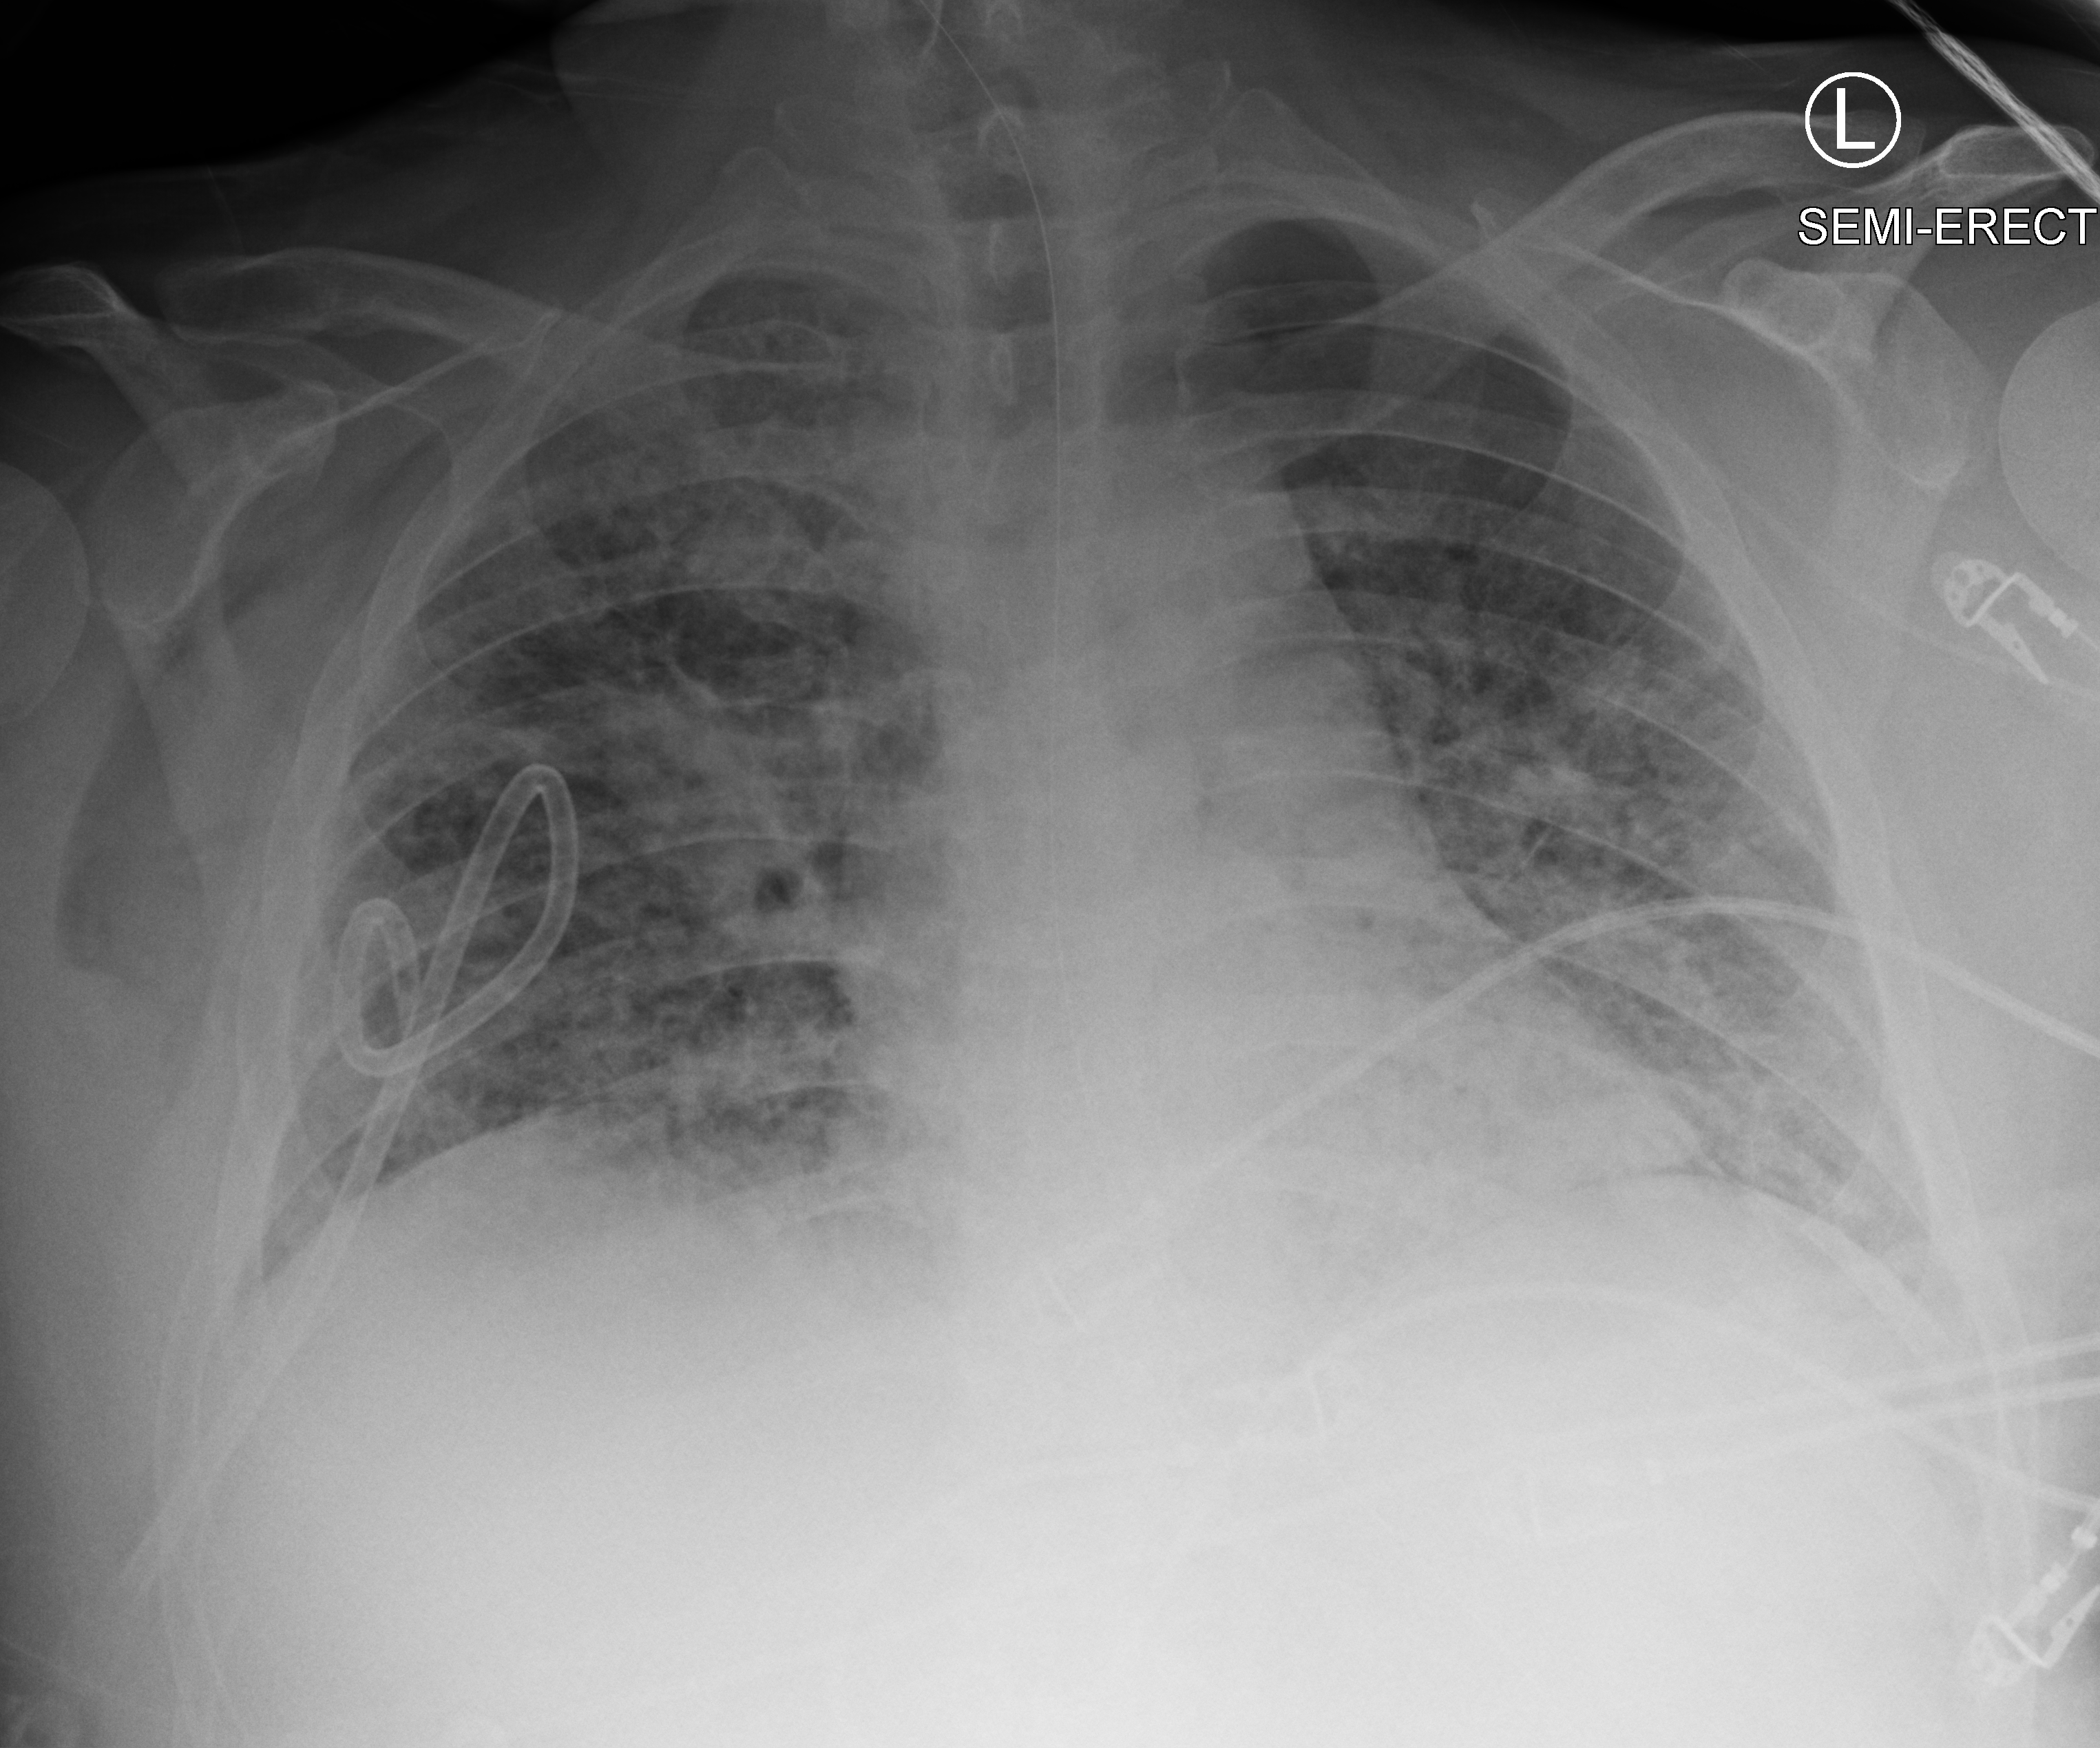
Chest X-ray (portable); anteroposterior (AP) projection. Adult patient hospitalised with COVID-19, age 18–59 years.
Admission-level facts for this patient (not findings on this image; timing relative to this image not recorded): mechanically ventilated during this hospital stay: yes.